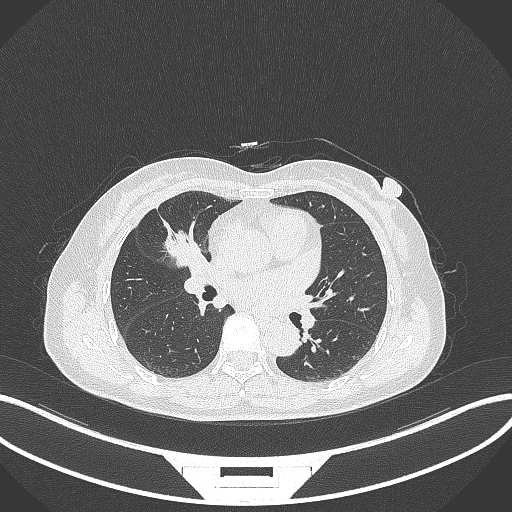
Chest CT, one axial slice; slice 157 of 284 in the series (ordered by position); reconstruction kernel B70f; 120 kVp; lung window (W 1500 / L -600 HU); 1 mm slice thickness; 512 × 512 image matrix. Female patient, age 51 years. From the clinical record (not read from this slice): clinical TNM (as recorded): T1c N0 M0.
Annotated regions visible in this slice (rectangle marked by the reading radiologist):
- lung tumour (recorded histology: adenocarcinoma): bounding box (x1, y1, x2, y2) in pixels: (165, 225, 201, 269)